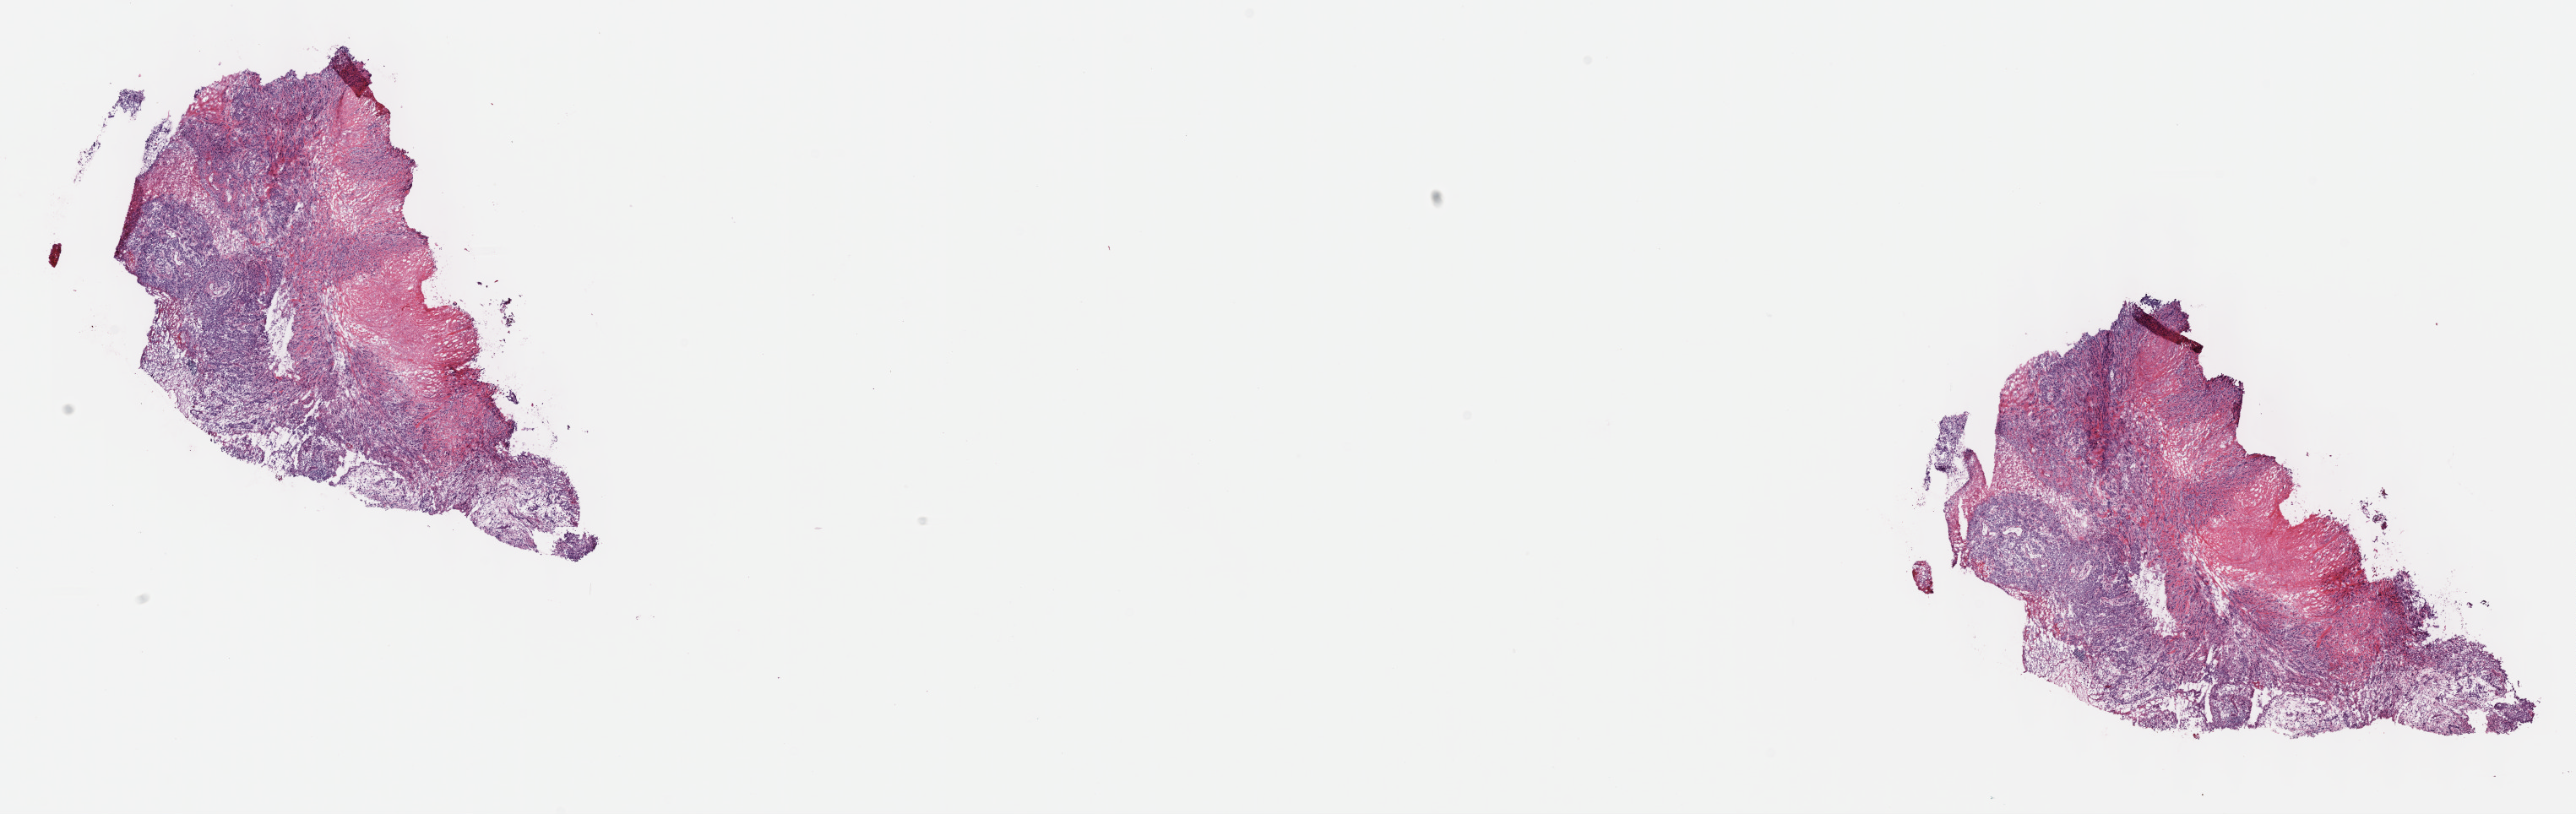
Whole-slide histology image, H&E, a low-resolution overview of the entire scanned area, about 24.7 x 7.8 mm (from a 40x scan), frozen section, head and neck, primary tumour sample. Male patient; age at initial diagnosis 71 years.
Pathologic diagnosis: Squamous cell carcinoma, NOS (cheek mucosa).